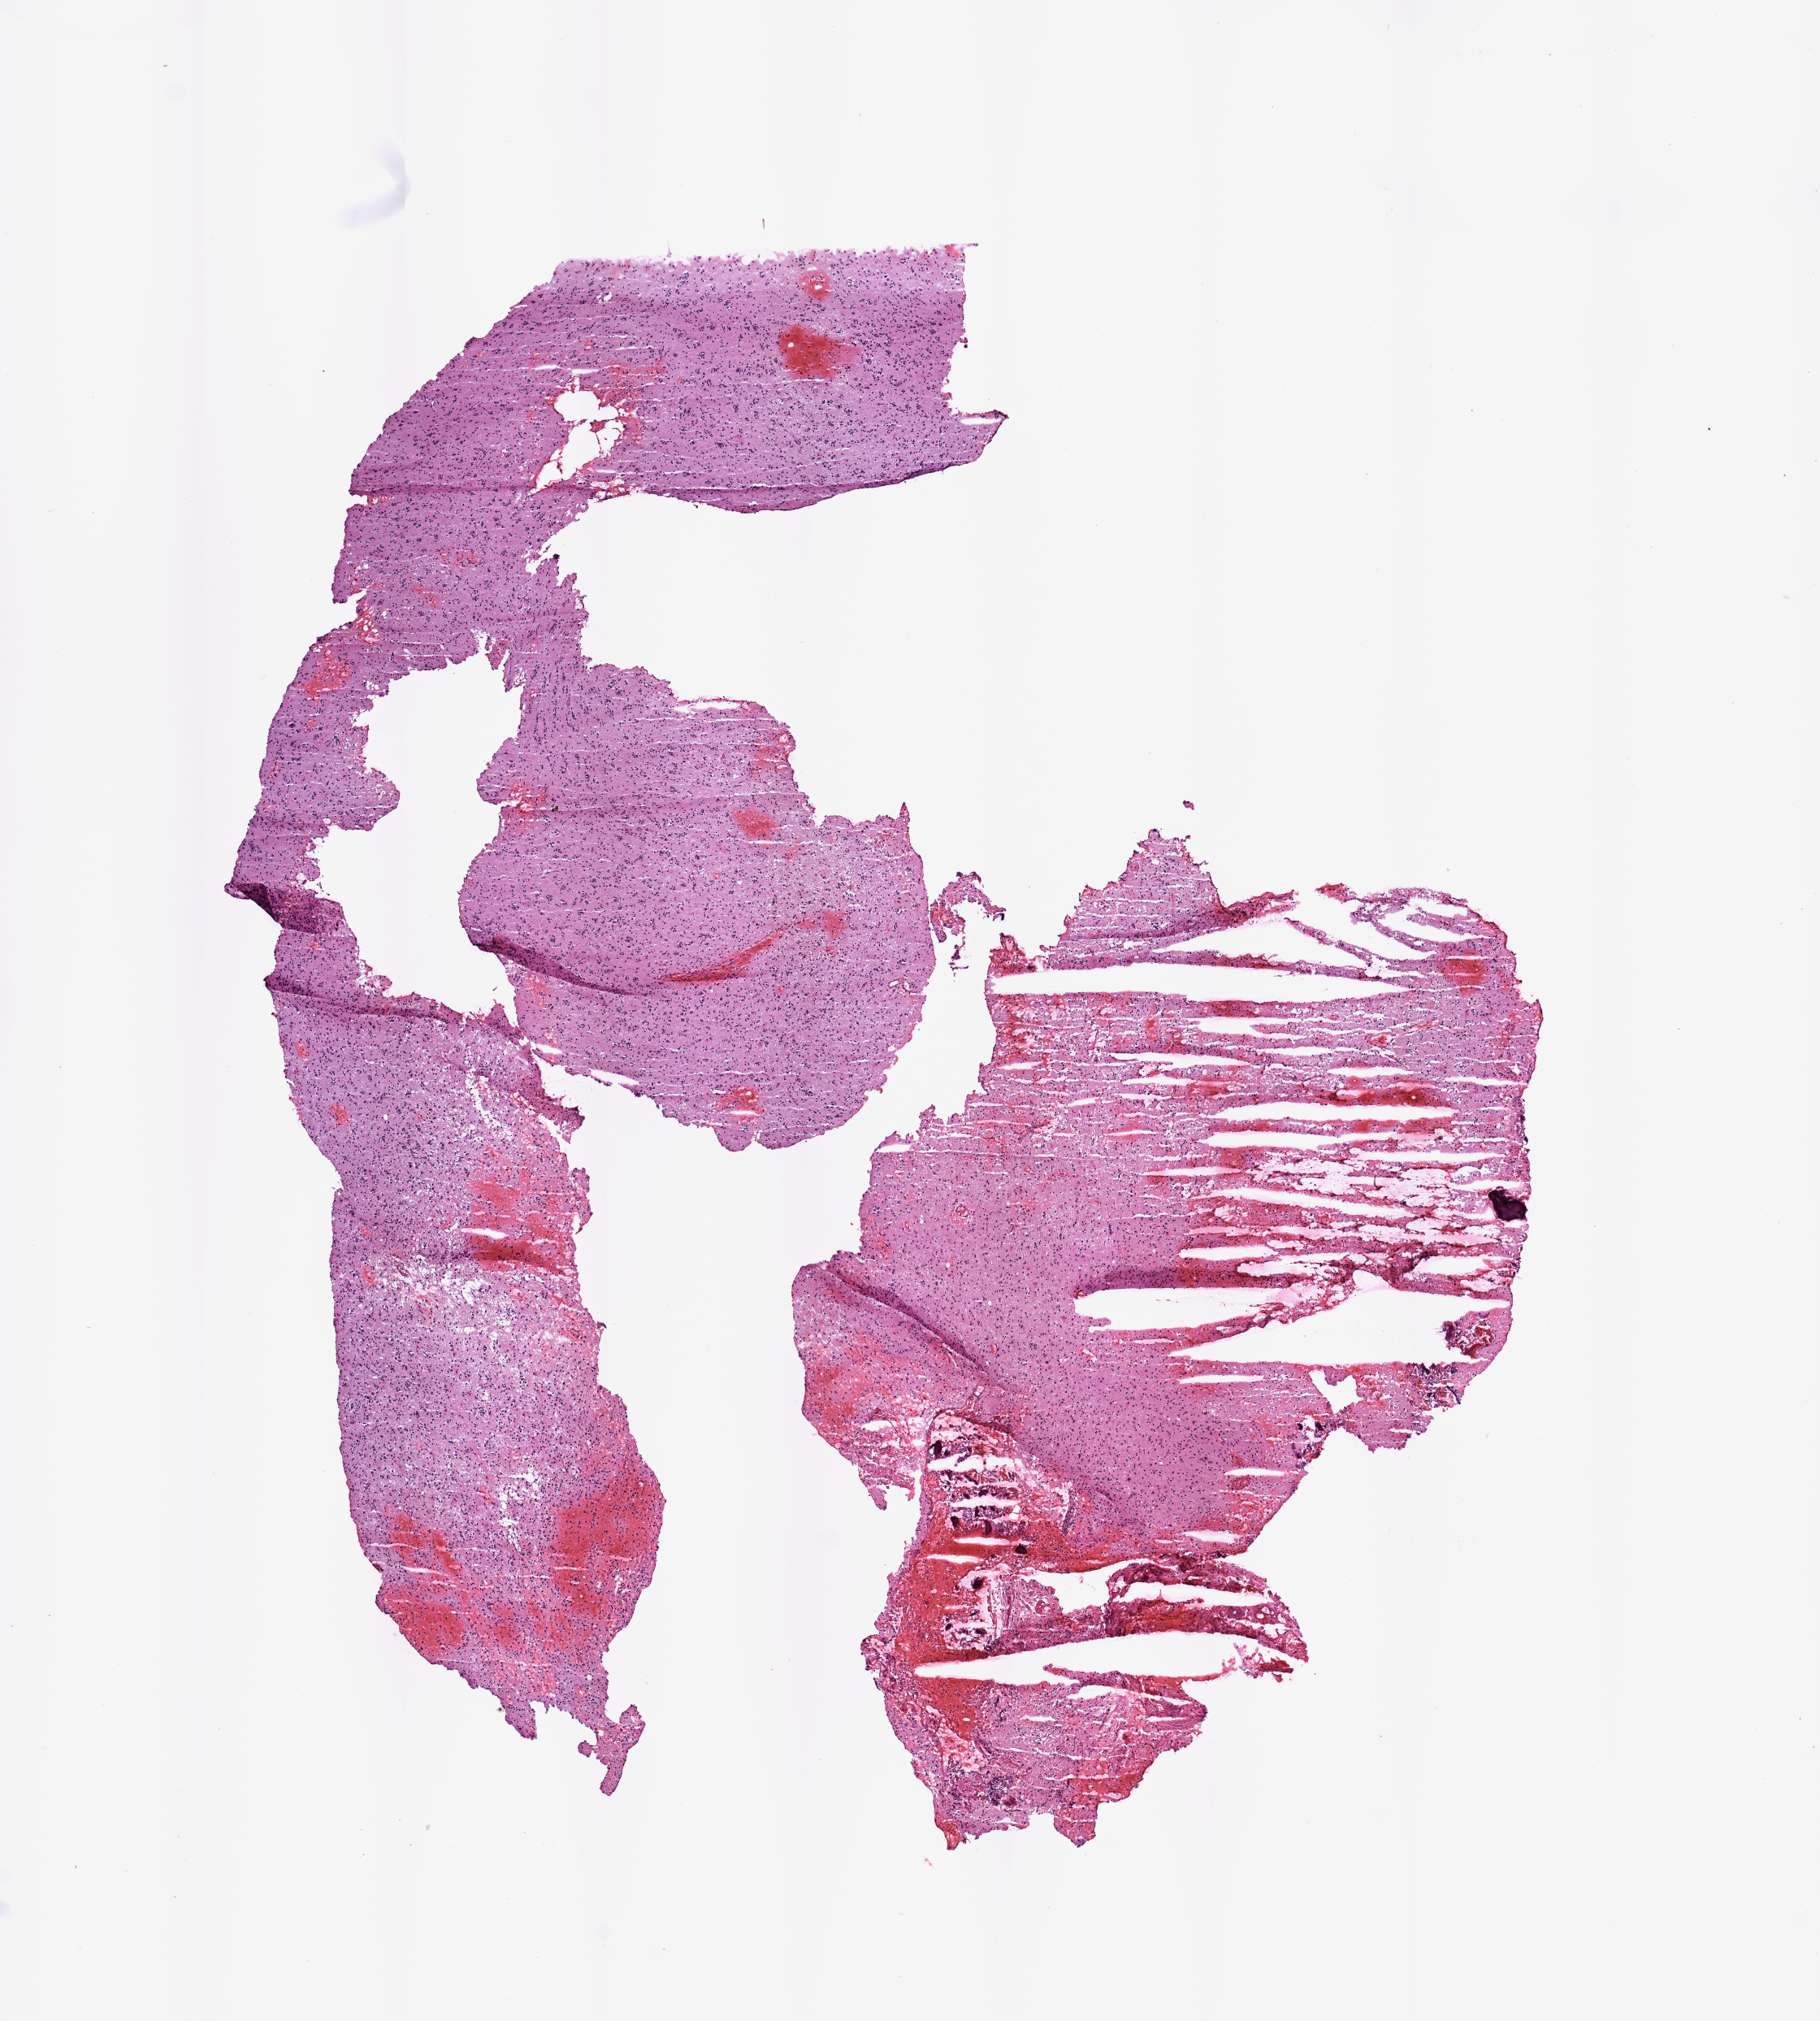
H&E whole-slide image — whole scanned area (about 8.9 x 9.8 mm) shown as a low-resolution overview. Tumour tissue sample, brain. 51-year-old male patient.
Patient diagnosis (cohort enrolment): glioblastoma multiforme (brain).